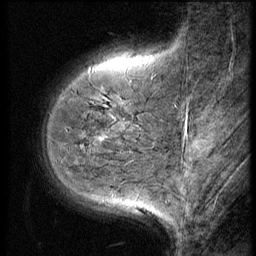
Breast MRI (dynamic contrast-enhanced), one sagittal slice. Slice 14 of 56 in the series (ordered by position). 3 images stored at this slice position (order not interpretable as contrast timing). 1.5 T. TE 4.2 ms, TR 9 ms. 2.5 mm slice thickness. 256 × 256 image matrix, field of view 180 × 180 mm. Patient: female, 49 years. Case-level facts recorded for this patient, not image findings: setting: breast cancer imaged before/during neoadjuvant chemotherapy; receptor status: HER2-positive.
Outlined on this slice (semi-automatically segmented with operator editing):
- analysis volume of interest (the breast-tissue region the enhancement analysis was run in; not a lesion): bounding box (x1, y1, x2, y2) in pixels: (39, 74, 148, 198)
- tumour enhancement mask (voxels above the 140 % enhancement threshold inside the analysis volume of interest): (98, 136, 105, 142)